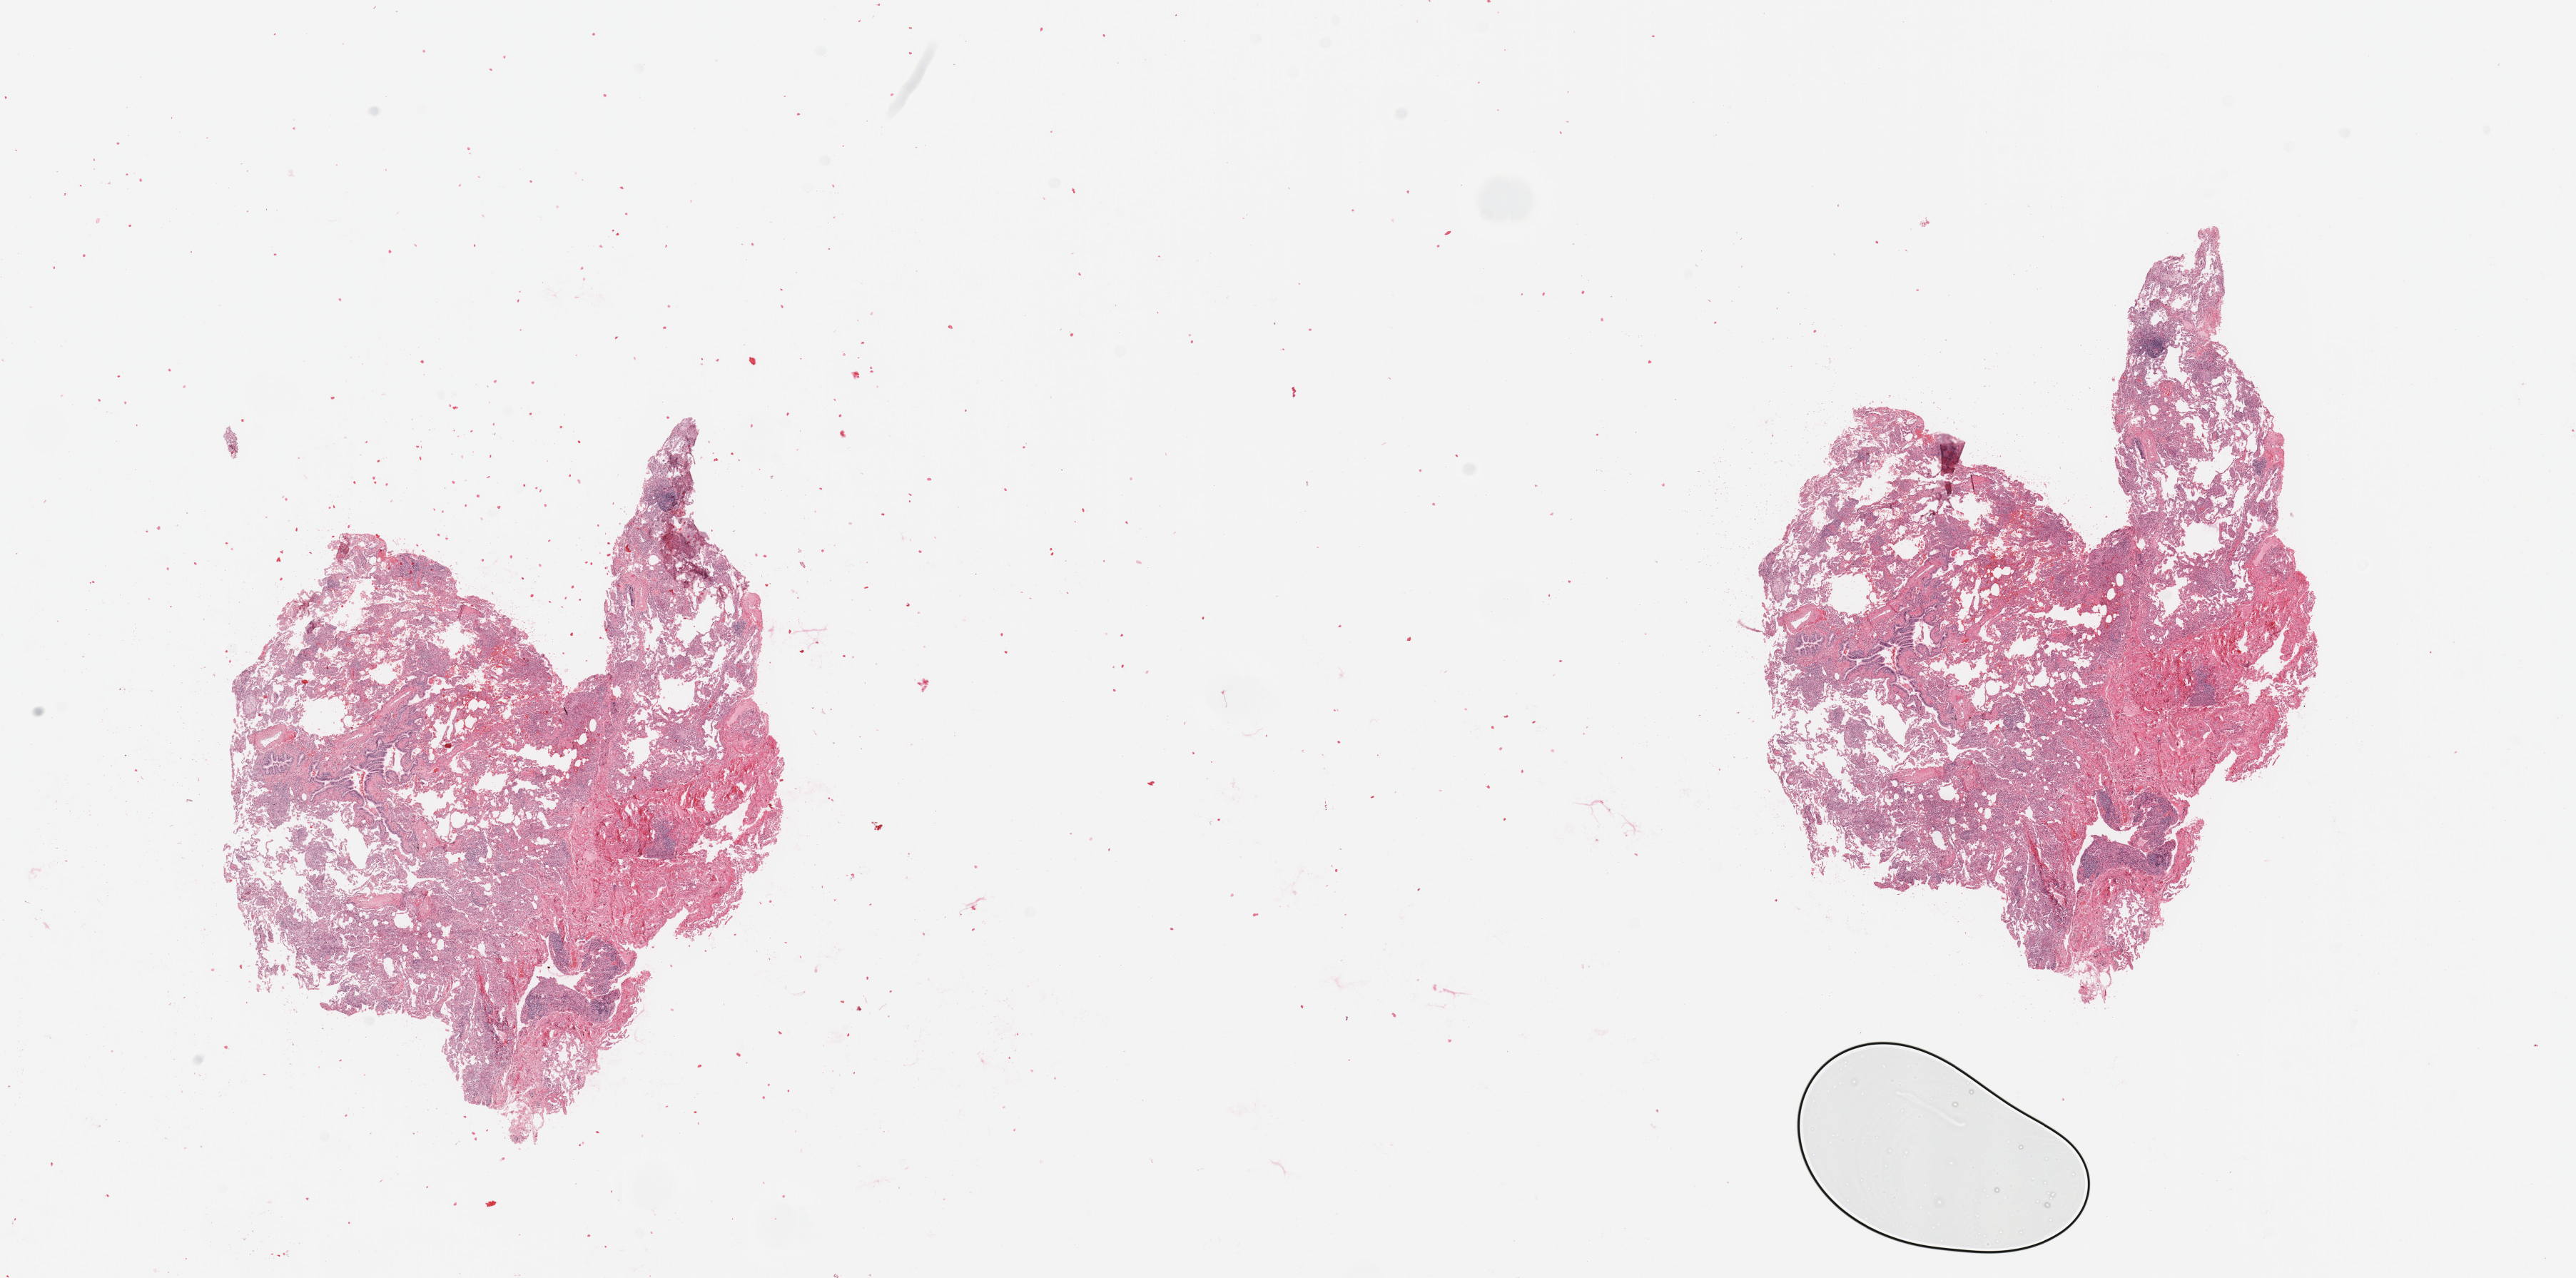
Hematoxylin and eosin (H&E) stained whole-slide image — a low-resolution overview of the entire scanned area, about 28.5 x 14.2 mm, lung, normal (non-tumour) tissue. Female, 77 y/o.
• this section: normal (non-tumour) tissue from the same patient
• patient diagnosis: Squamous cell carcinoma, NOS